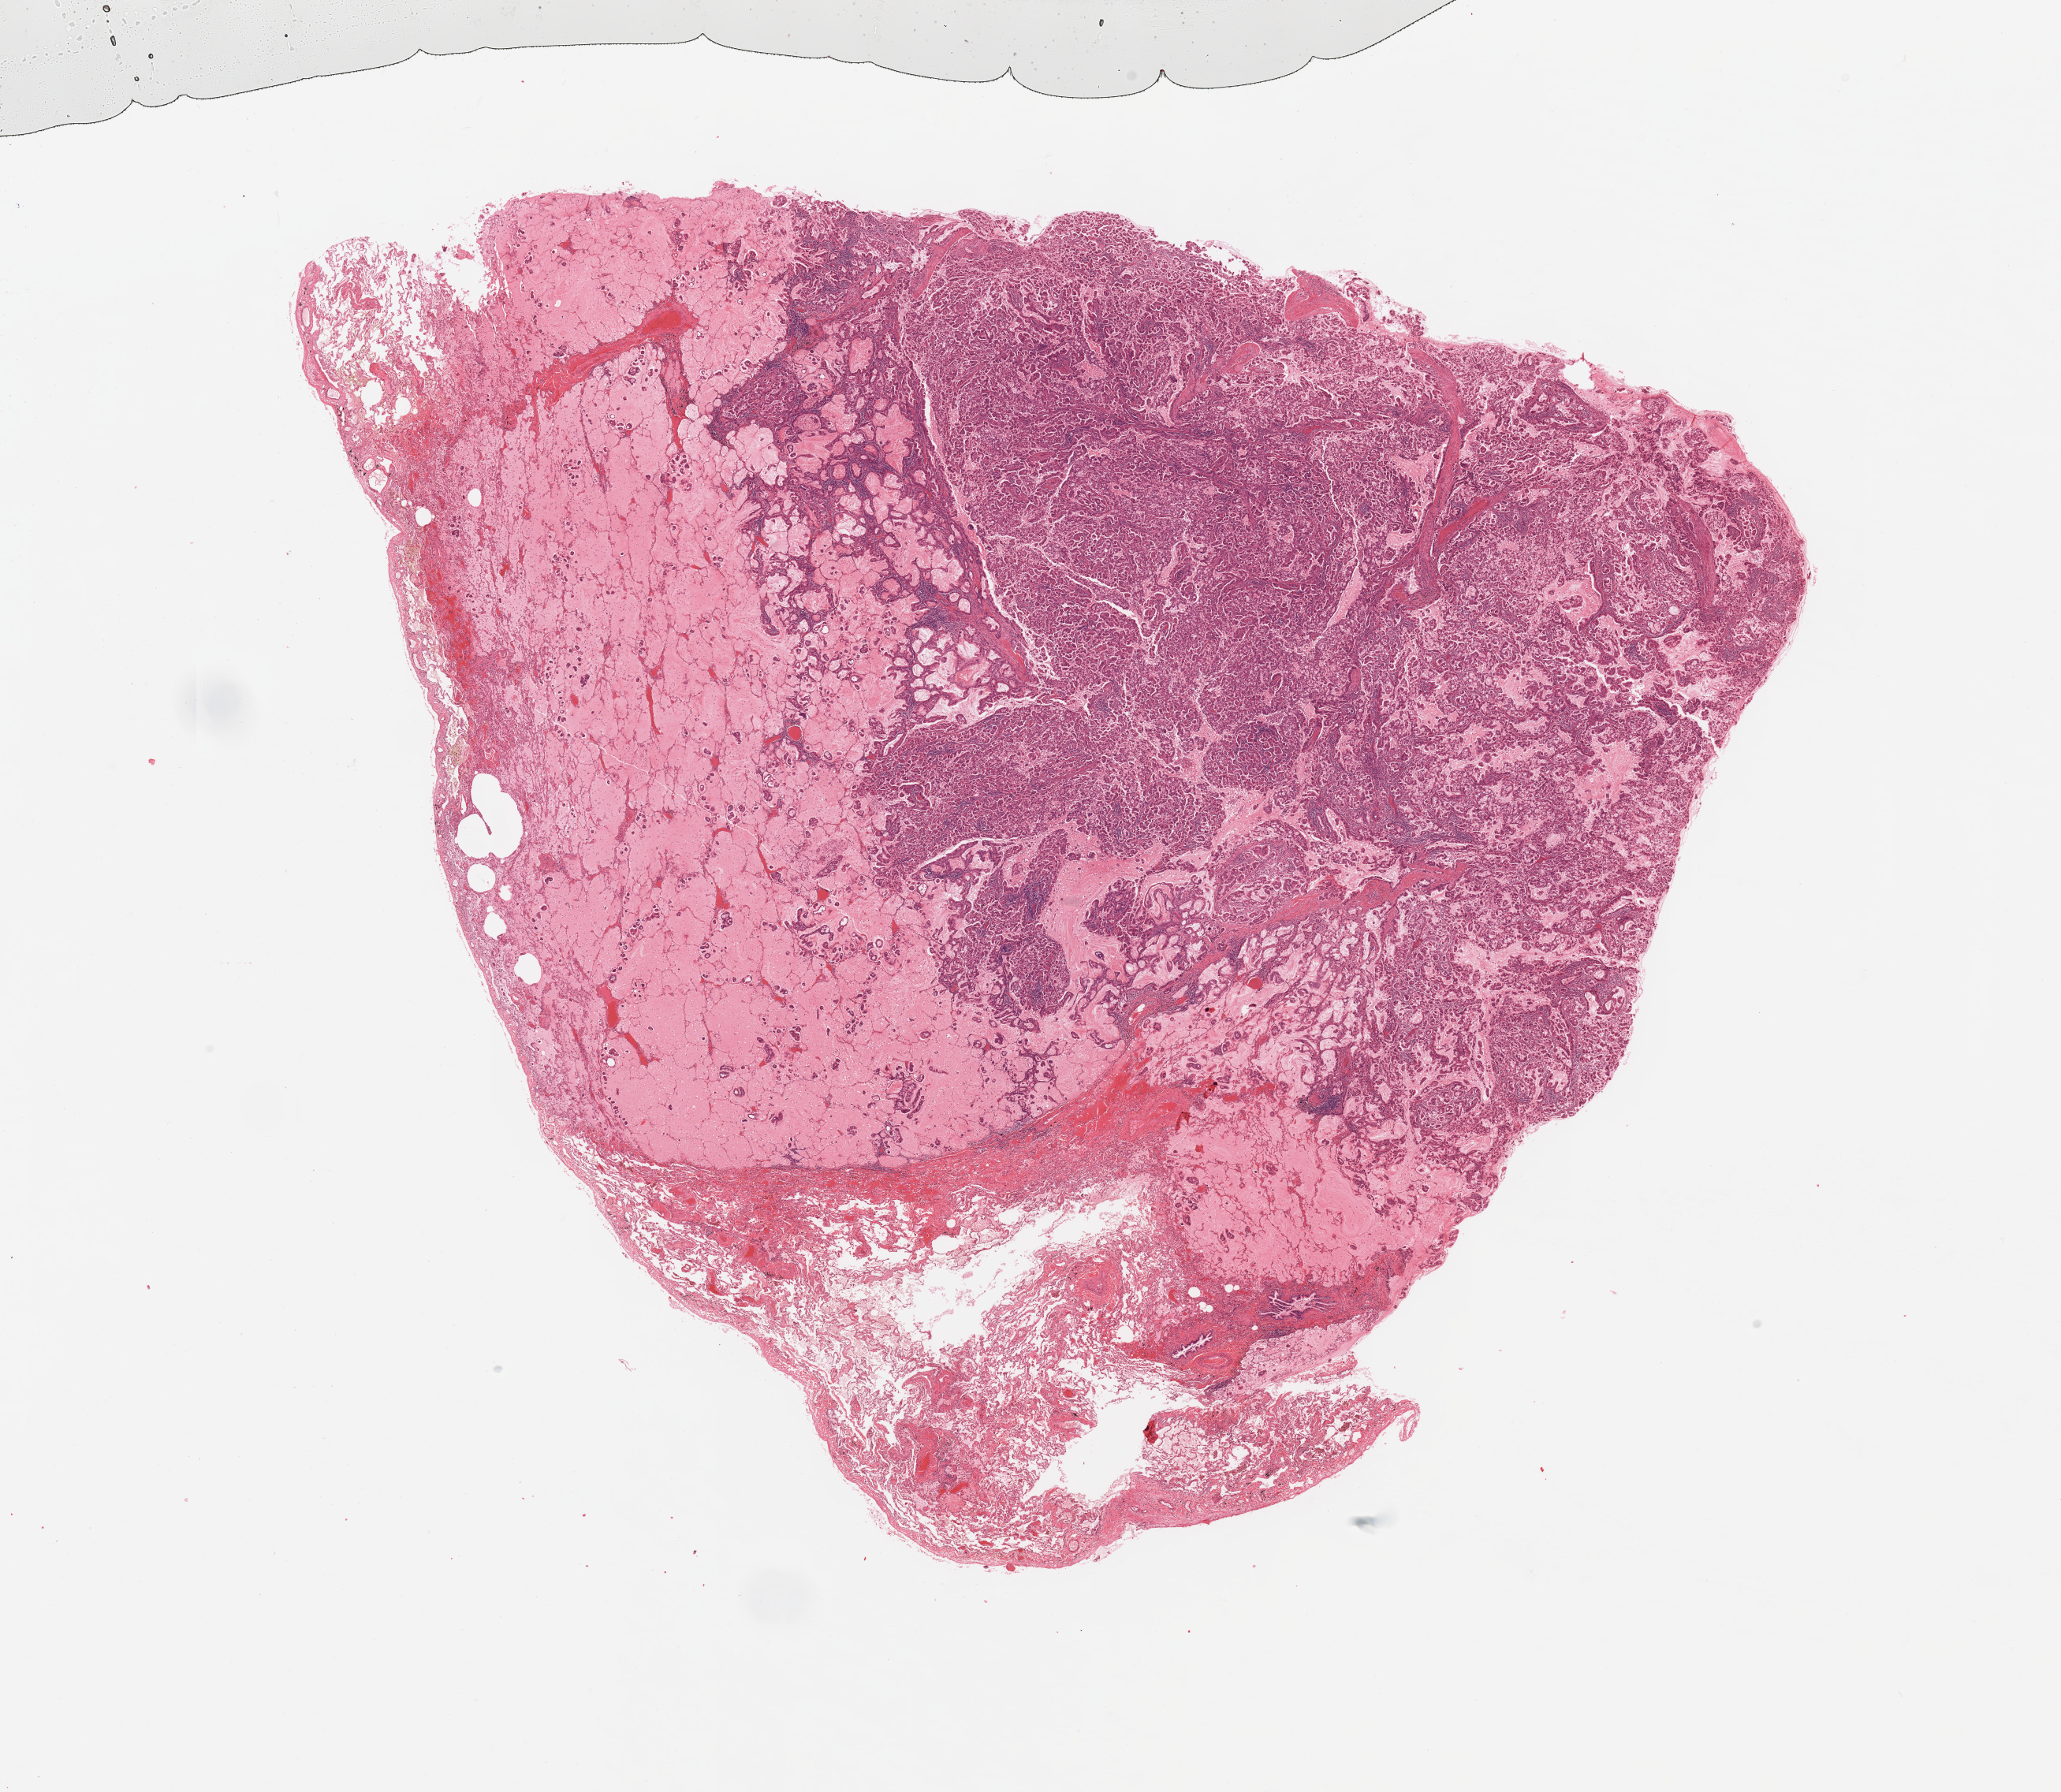
H&E-stained whole-slide image — whole scanned area (about 20.7 x 18.0 mm, from a 20x scan) shown as a low-resolution overview; tumour tissue sample, sampled site: lung. 52-year-old female patient. Histologic grade: G2 (moderately differentiated). Pathologist review of this section (percent, as recorded): tumour nuclei 80%, necrosis 5%.
* primary tumour site (as recorded): left lower lobe
* AJCC pathologic stage: IIA
* histologic diagnosis: Adenocarcinoma, NOS